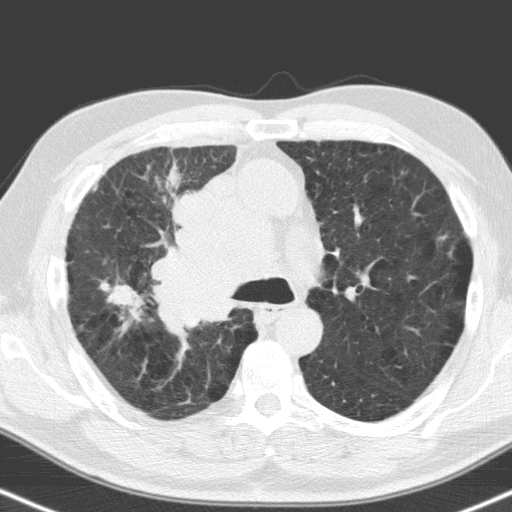
Low-dose screening chest CT, one axial slice. Slice 110 of 160 in the series (ordered by position). 120 kVp. Lung window (W 1500 / L -600 HU). 3.2 mm slice thickness. 512 × 512 image matrix, field of view 324 × 324 mm.
Annotated regions visible in this slice (manually delineated by an expert):
- lesion 1 (tumor, hilum of right lung): bounding box (x1, y1, x2, y2) in pixels: (154, 177, 259, 325)
- lesion 2 (tumor, upper lobe of right lung): (109, 284, 138, 307)